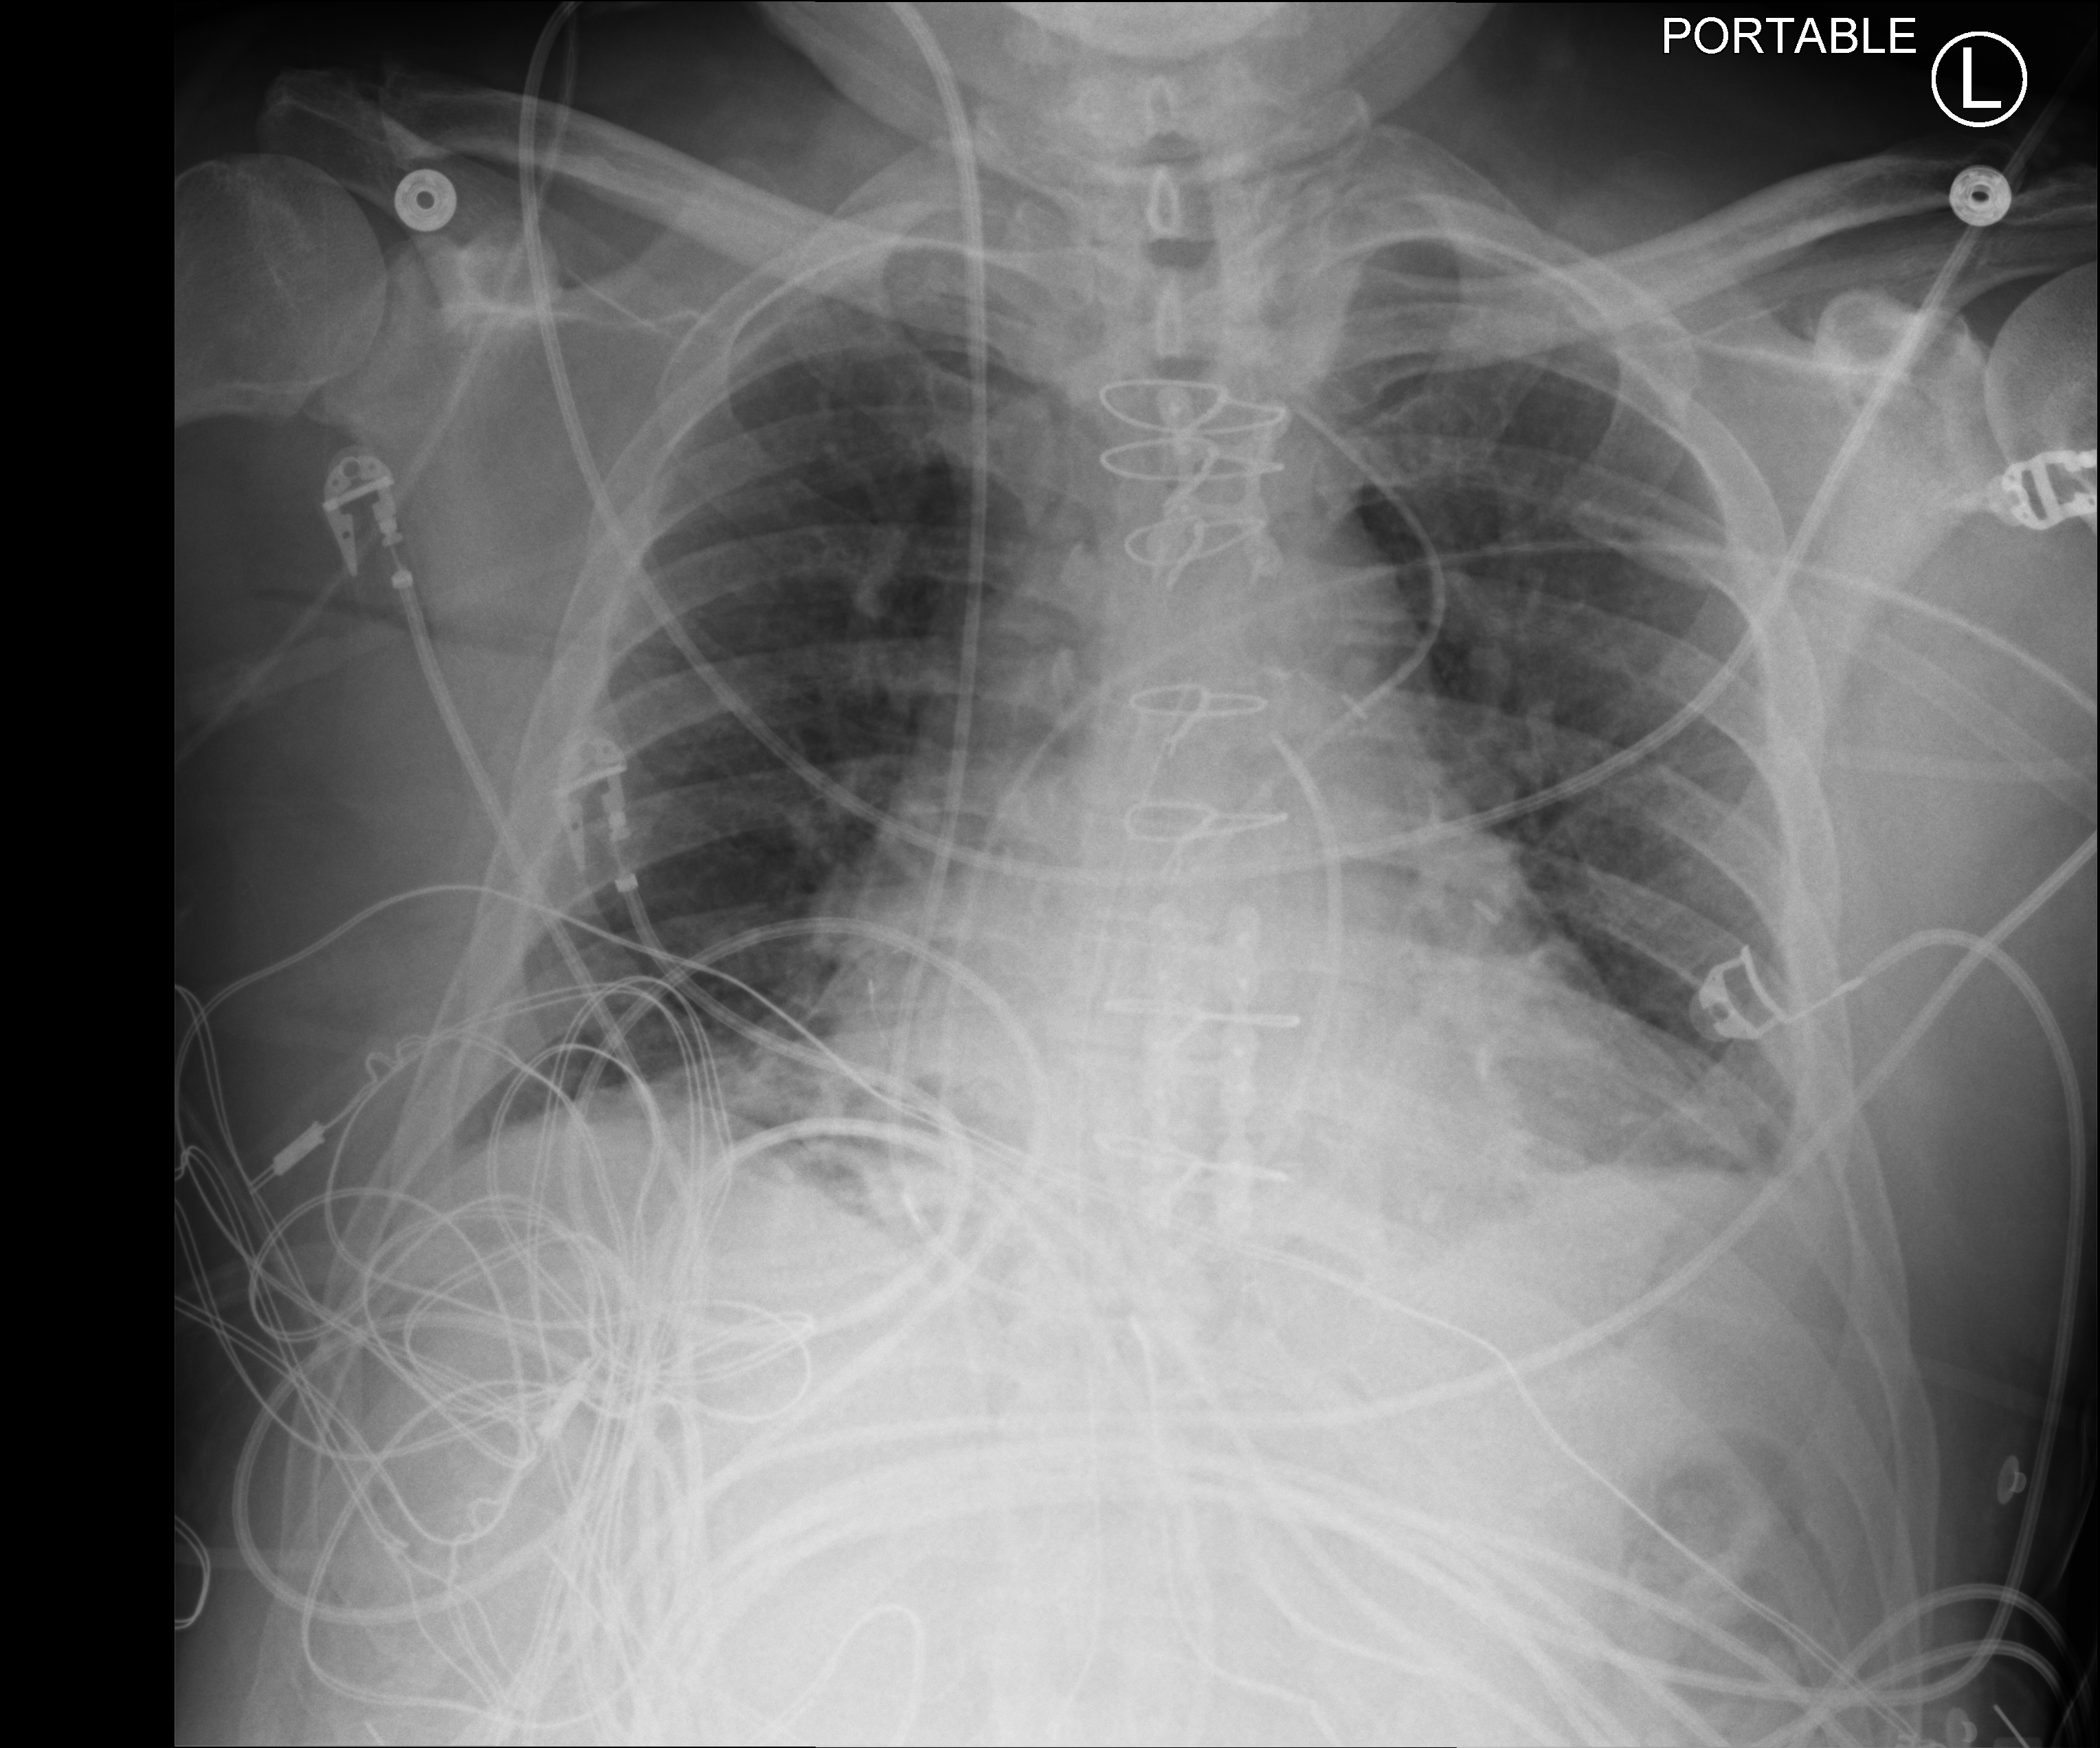
Bedside chest radiograph (computed radiography). Male patient hospitalised with COVID-19, age 60–74 years.
From the hospital-stay record, not from the radiograph (when in the stay this image was taken is not recorded): chronic kidney disease (admission record): no; mechanically ventilated during this hospital stay: no; admitted to intensive care during this hospital stay: no.